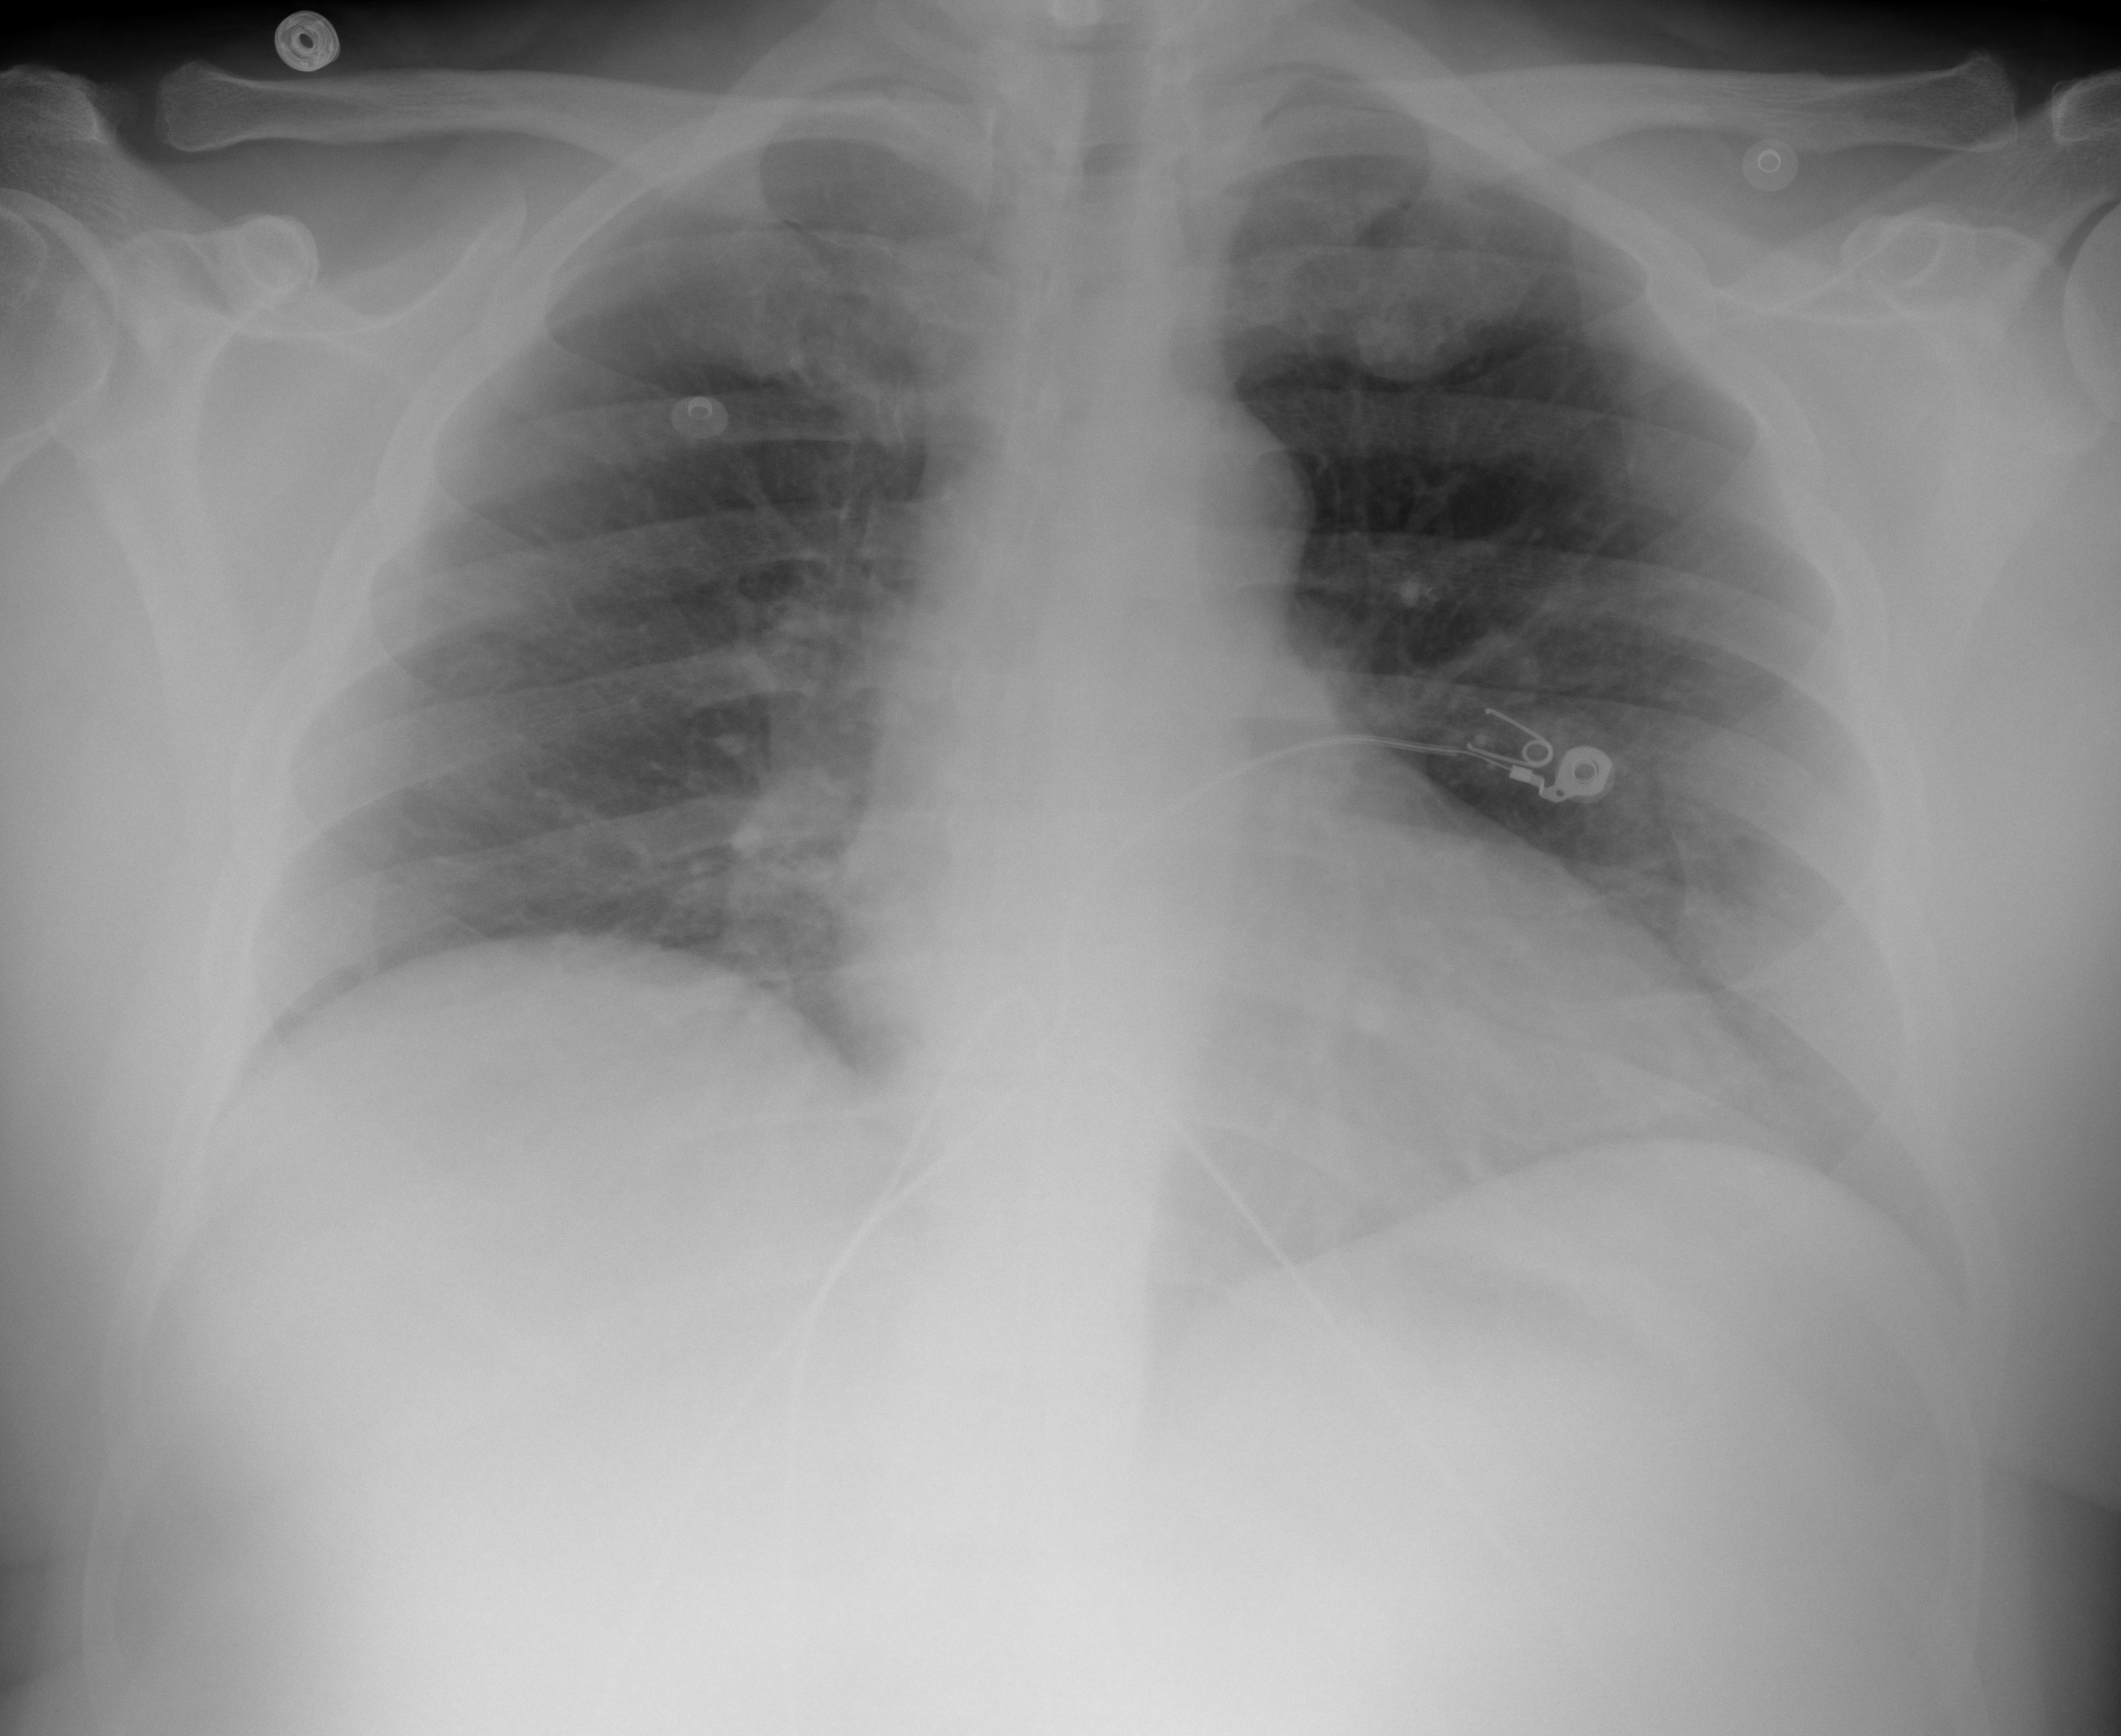
Portable chest radiograph, AP projection. Male patient, age 55 years; COVID-19 (test-positive).
Radiologist key findings (as recorded): The lungs are clear and without focal consolidation.